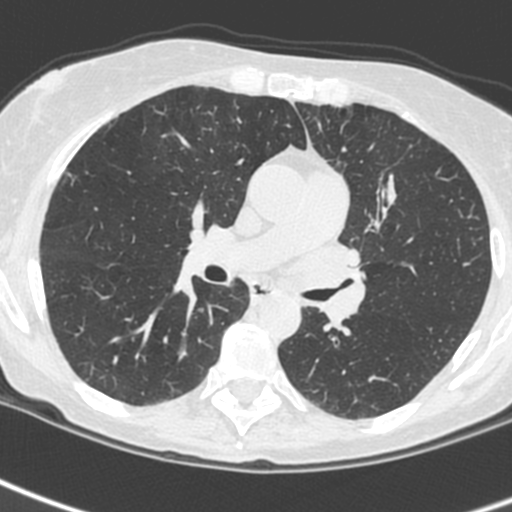
Low-dose screening chest CT, one axial slice. Position 141 of 242 along the scan axis. 120 kVp. Lung window (W 1500 / L -600 HU). 1.3 mm slice thickness. 512 × 512 image matrix, field of view 284 × 284 mm.
Structures marked on this image (expert manual segmentation):
- lesion 3 (tumor, upper lobe of left lung): box from (x=293, y=239) to (x=365, y=321) px